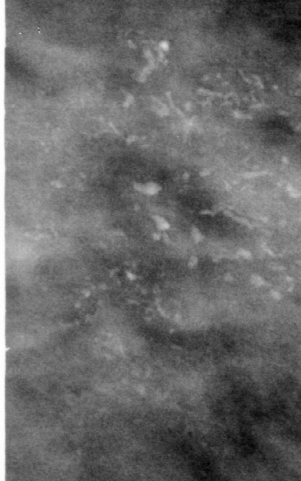
Cropped region of a digitized screen-film mammogram centred on a radiologist-marked abnormality; left breast; MLO view; BI-RADS breast density category 3 (scale 1–4).
- Calcifications, morphology fine linear branching, distribution clustered; BI-RADS assessment category 5; pathology result (as recorded, not read from the image): malignant.